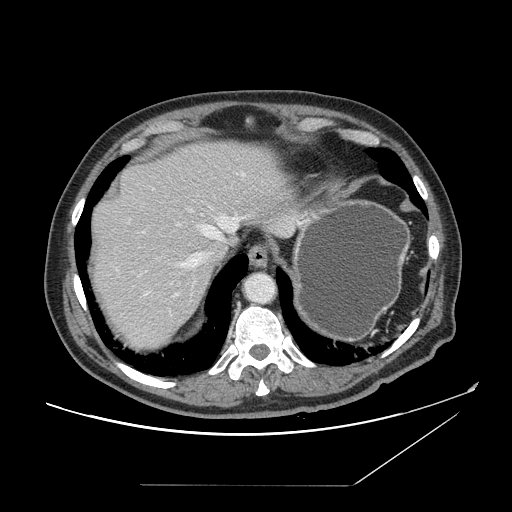
Contrast-enhanced abdominal CT, one axial slice. Slice 128 of 166 in the series (ordered by position). 120 kVp. Intravenous contrast given. Soft-tissue window (W 400 / L 40 HU). 2.5 mm slice thickness. 512 × 512 image matrix, field of view 416 × 416 mm. Male patient, age 80 years. From the clinical record (not read from this slice): diagnosis: colorectal cancer liver metastases, imaged before liver resection; multiple liver metastases: no; largest metastasis: 2.2 cm; disease in both lobes: no.
Structures marked on this image (expert manual segmentation):
- hepatic veins: box from (x=177, y=209) to (x=243, y=270) px
- liver: (x=91, y=141)–(x=295, y=349)
- planned liver remnant (the part of the liver to remain after resection): (x=91, y=141)–(x=293, y=256)
- portal vein (with intrahepatic branches): (x=143, y=210)–(x=194, y=233)